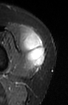
MRI of an extremity soft-tissue mass, one axial slice; position 35 of 52 along the scan axis; STIR; MR volume resampled by the dataset authors to the PET/CT grid (not the native acquisition matrix); 3.27 mm slice thickness; 68 × 105 image matrix. Female patient. Case-level facts recorded for this patient, not image findings: histological type: spindle cell suggestive of biphasic synovial sarcoma; grade: intermediate; site of the primary tumour: left knee.
Annotated regions visible in this slice (expert contour drawn on MRI and transferred to this co-registered scan by the dataset authors):
- gross tumour volume including surrounding oedema: box from (x=21, y=29) to (x=45, y=69) px
- gross tumour volume (mass): (x=21, y=29)–(x=45, y=69)